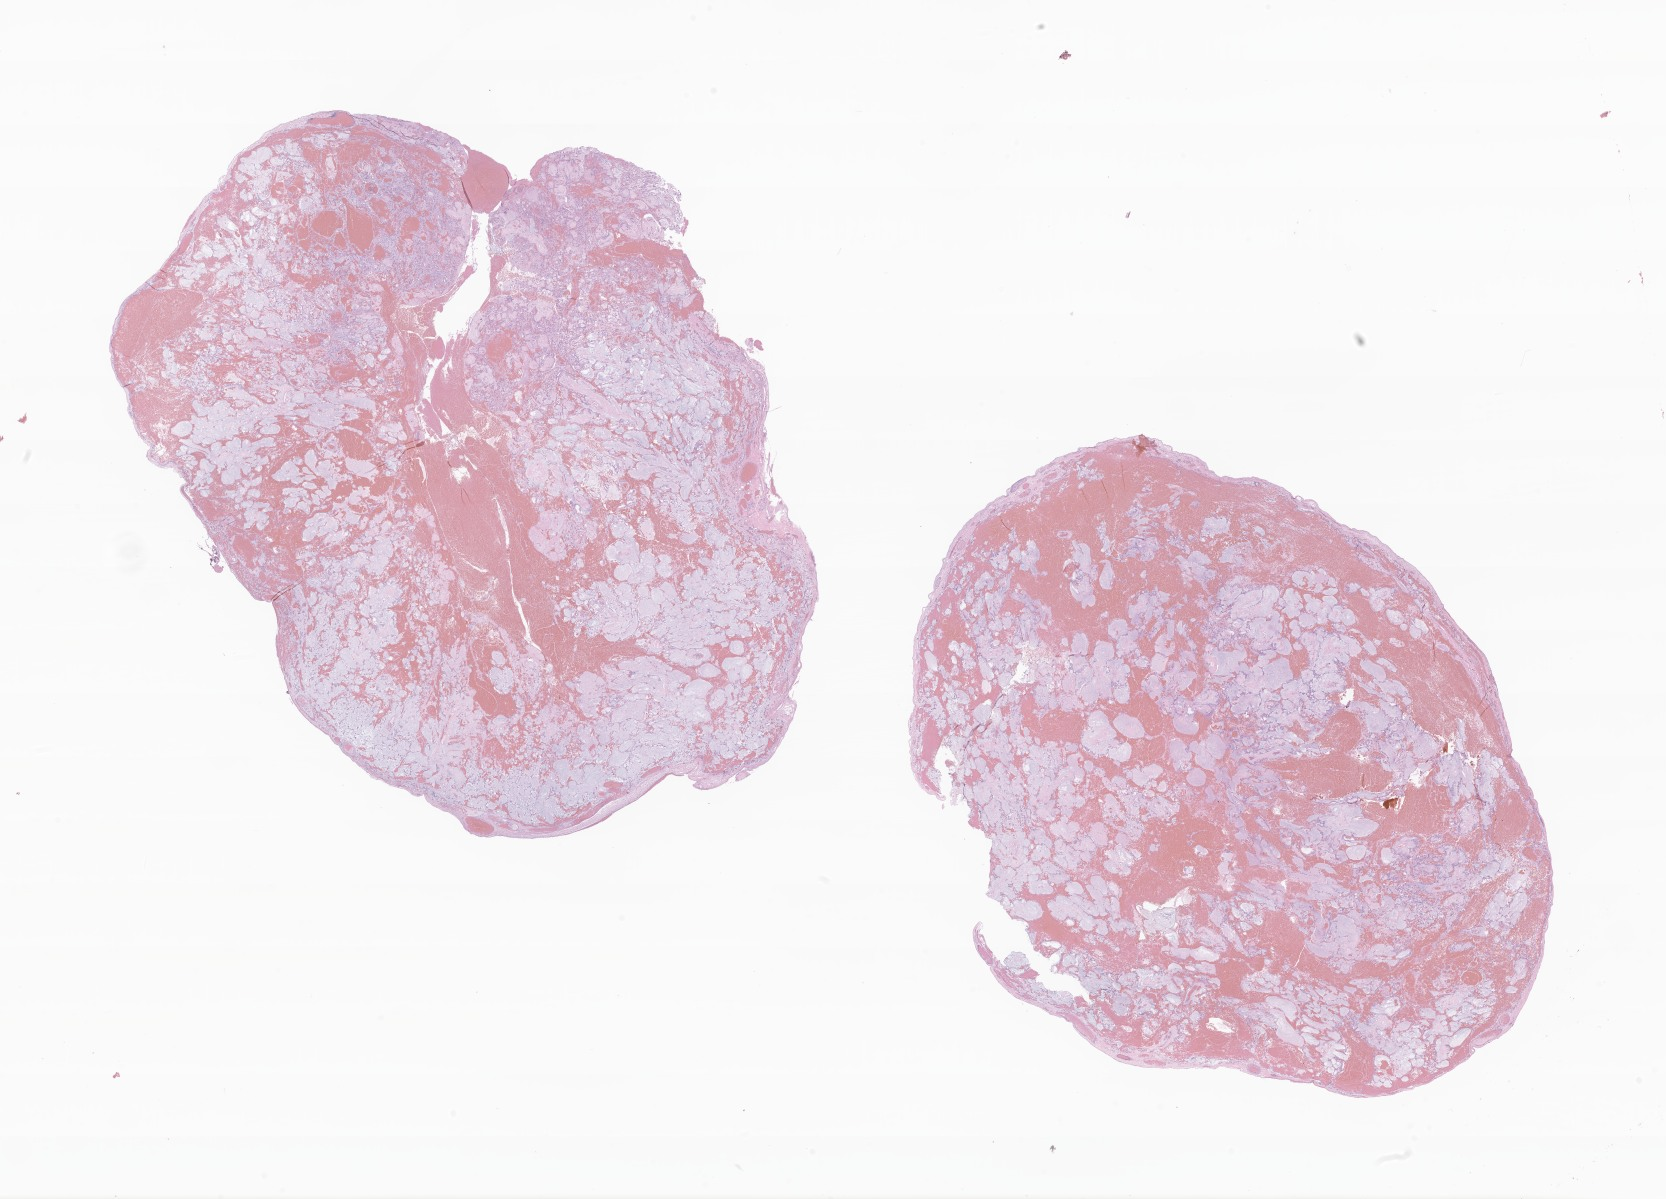
H&E whole-slide image of tumor tissue from the spinal cord, shown as a low-resolution overview of the whole scanned area (about 28.1 x 20.2 mm). FFPE section. Patient: male, age 204 months (17 years).
Diagnosis (ICD-O-3 morphology term): Myxopapillary ependymoma.